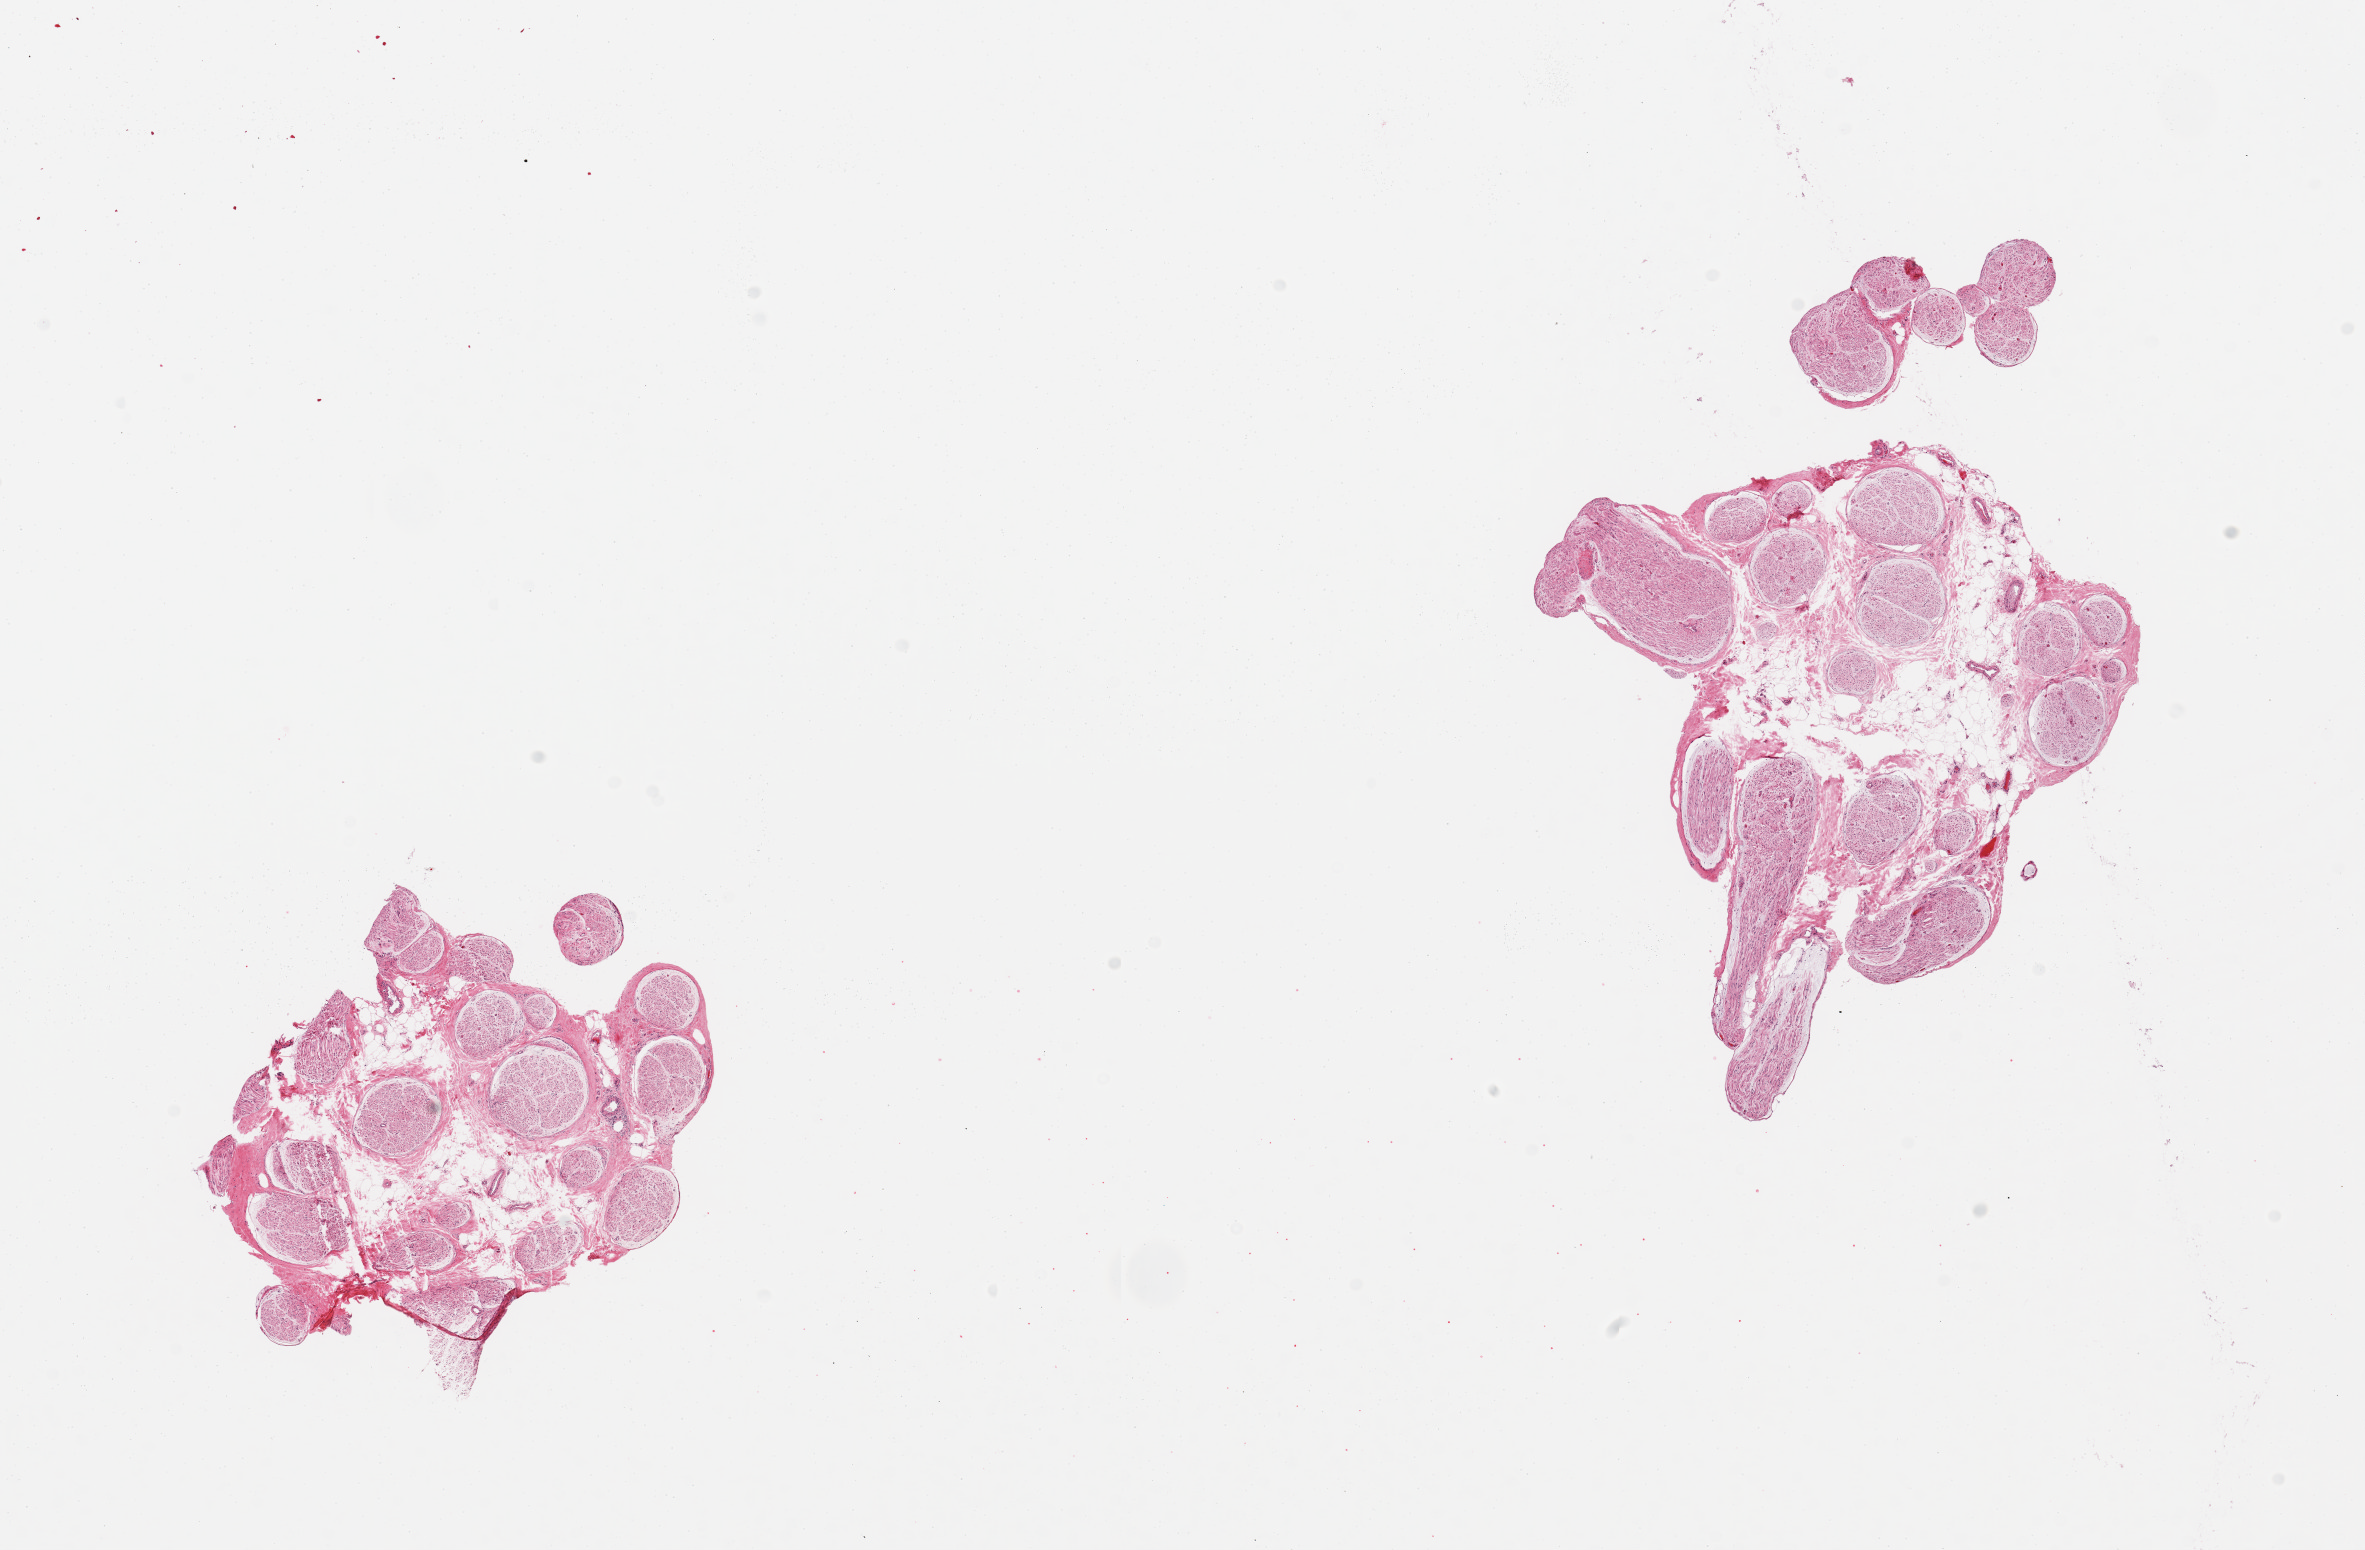
Whole-slide image, hematoxylin and eosin (H&E) stain, low-resolution overview of the scanned area, about 18.7 x 12.3 mm. PAXgene-fixed, paraffin-embedded tissue. Sampled site (target tissue): tibial nerve. Donor tissue sample. Male donor.
* pathologist's review note for this sample: 2 pieces, no significant adherent fat' moderate interstitial fat